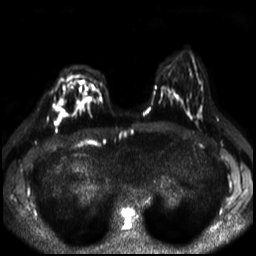
Breast MRI, one axial slice. Position 13 of 30 along the scan axis. Diffusion-weighted series; image 2 of 4 stored at this slice position (different b-values; order by instance number). 3 T. 4 mm slice thickness. 256 × 256 image matrix, field of view 320 × 320 mm. Female patient.
Annotated regions visible in this slice (expert manual segmentation):
- tumour on diffusion-weighted imaging: bounding box <56,101,66,124> (left, top, right, bottom; pixels)